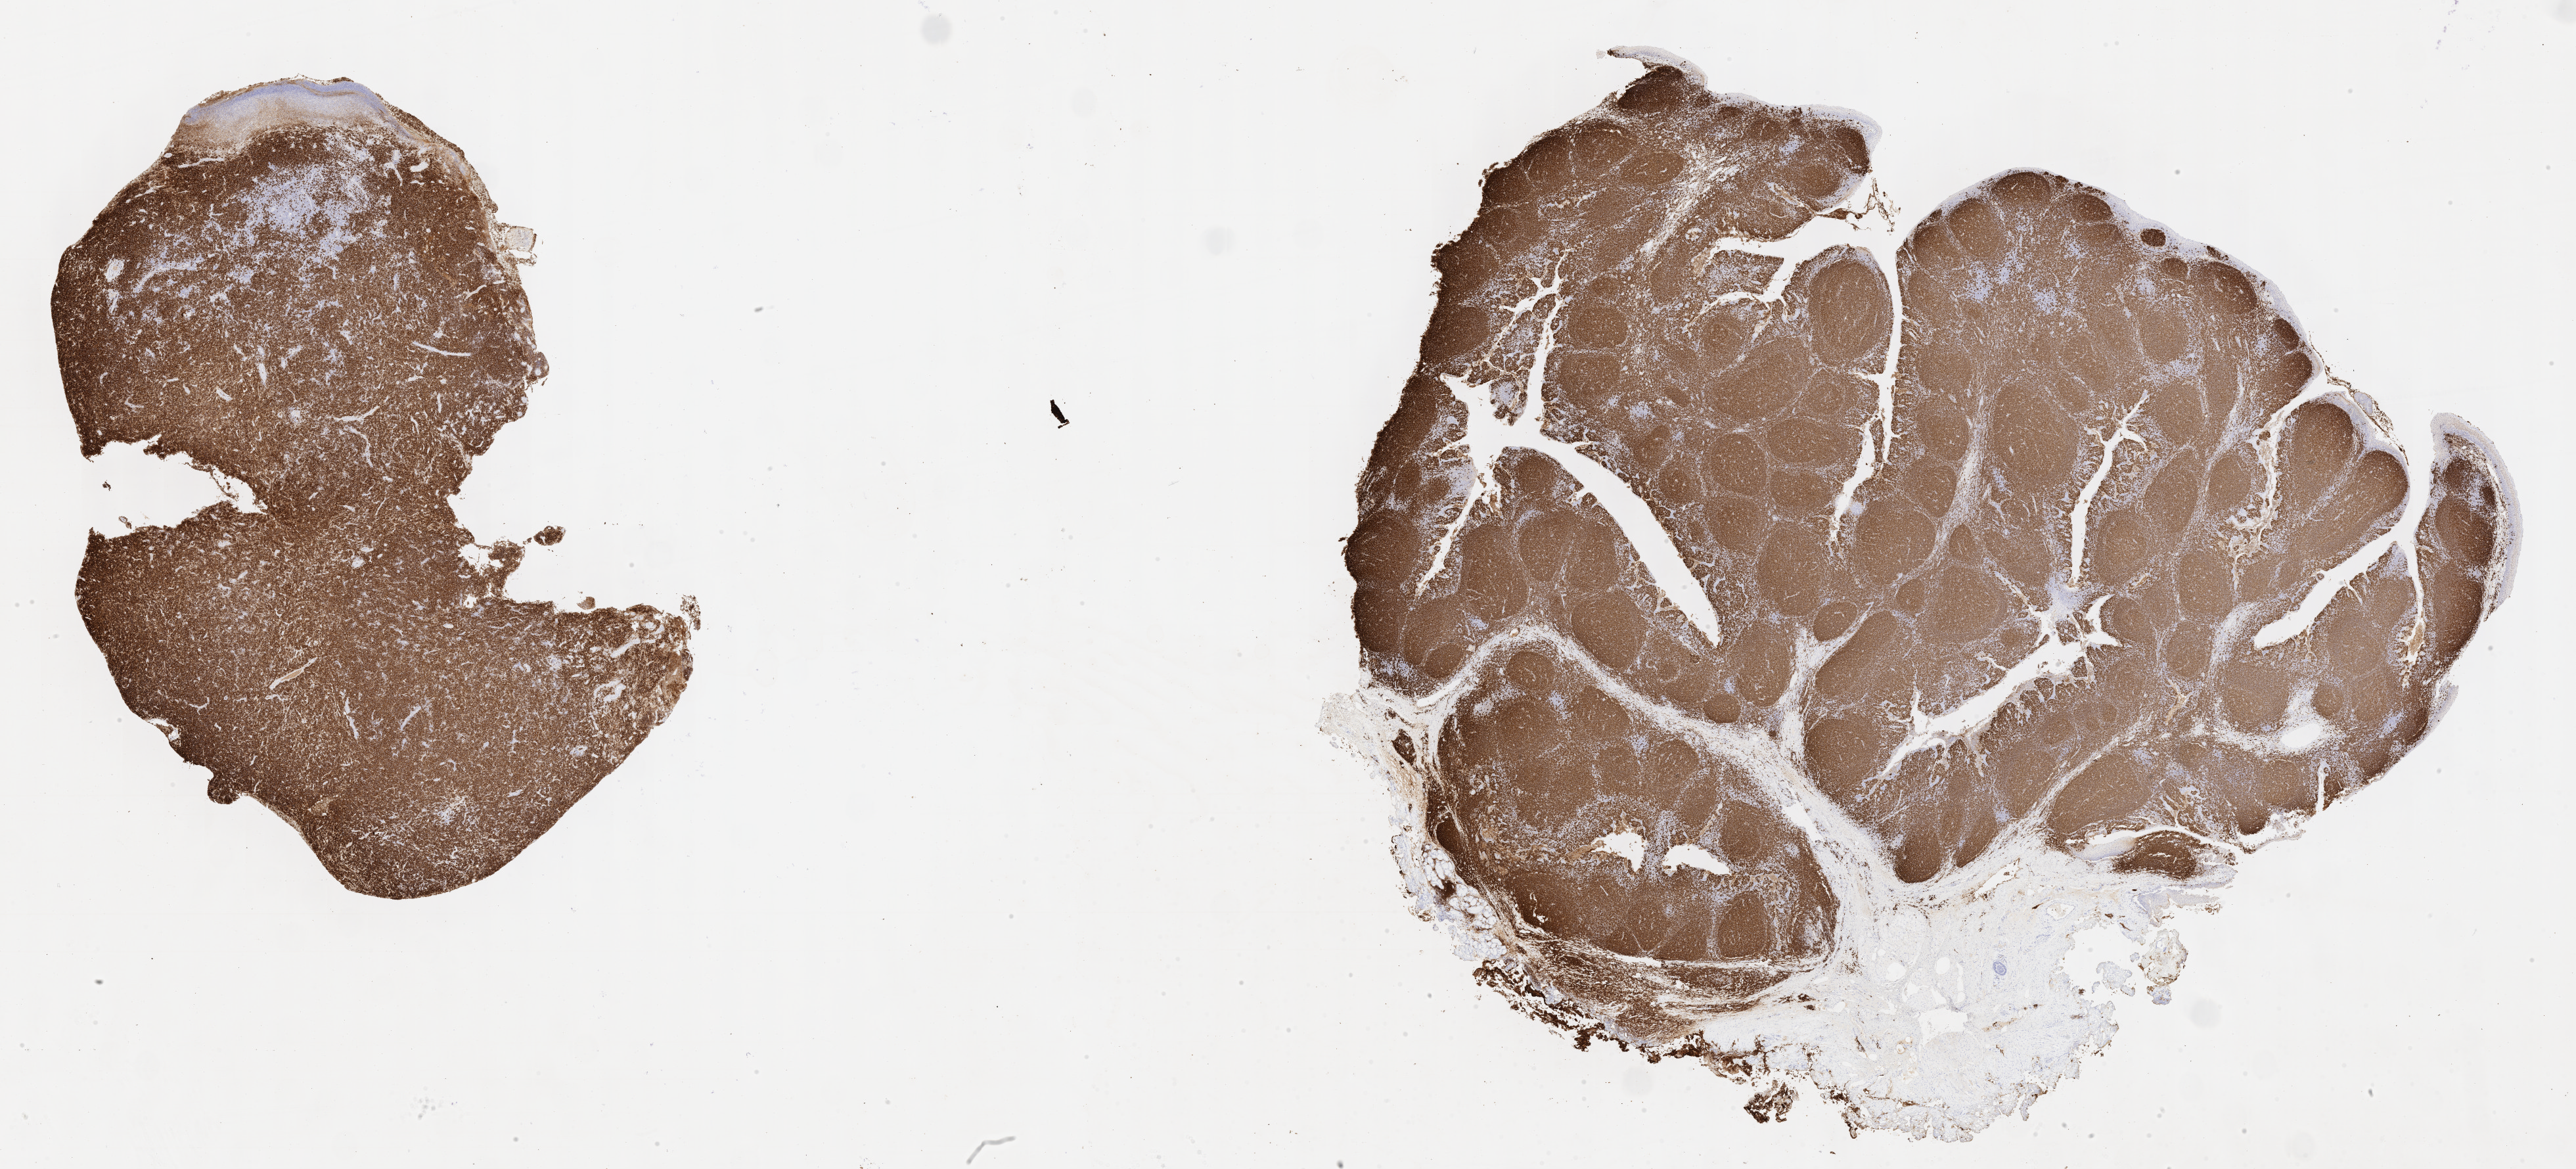
Whole-slide image, immunohistochemical stain for CD20 — whole scanned area (about 31.7 x 14.4 mm) shown as a low-resolution overview; tumor tissue. Male, age 7 years at initial diagnosis.
• diagnosis: Diffuse large B-cell lymphoma, NOS